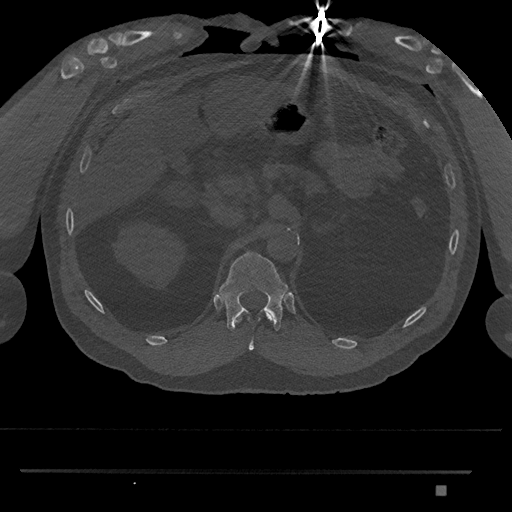
CT including the spine, one axial slice. Slice 905 of 1134 in the series (ordered by position). Reconstruction kernel Br40s/3. 120 kVp. Bone window (W 1800 / L 400 HU). 0.5 mm slice thickness. 512 × 512 image matrix, field of view 429 × 429 mm. Patient: male, 65 years. From the clinical record (not read from this slice): primary cancer: prostate.
Annotated regions visible in this slice (semi-automatic segmentation, software-assisted and operator-edited):
- T11 vertebra: bounding box <236,312,272,350> (left, top, right, bottom; pixels)
- T12 vertebra: <219,251,288,331>